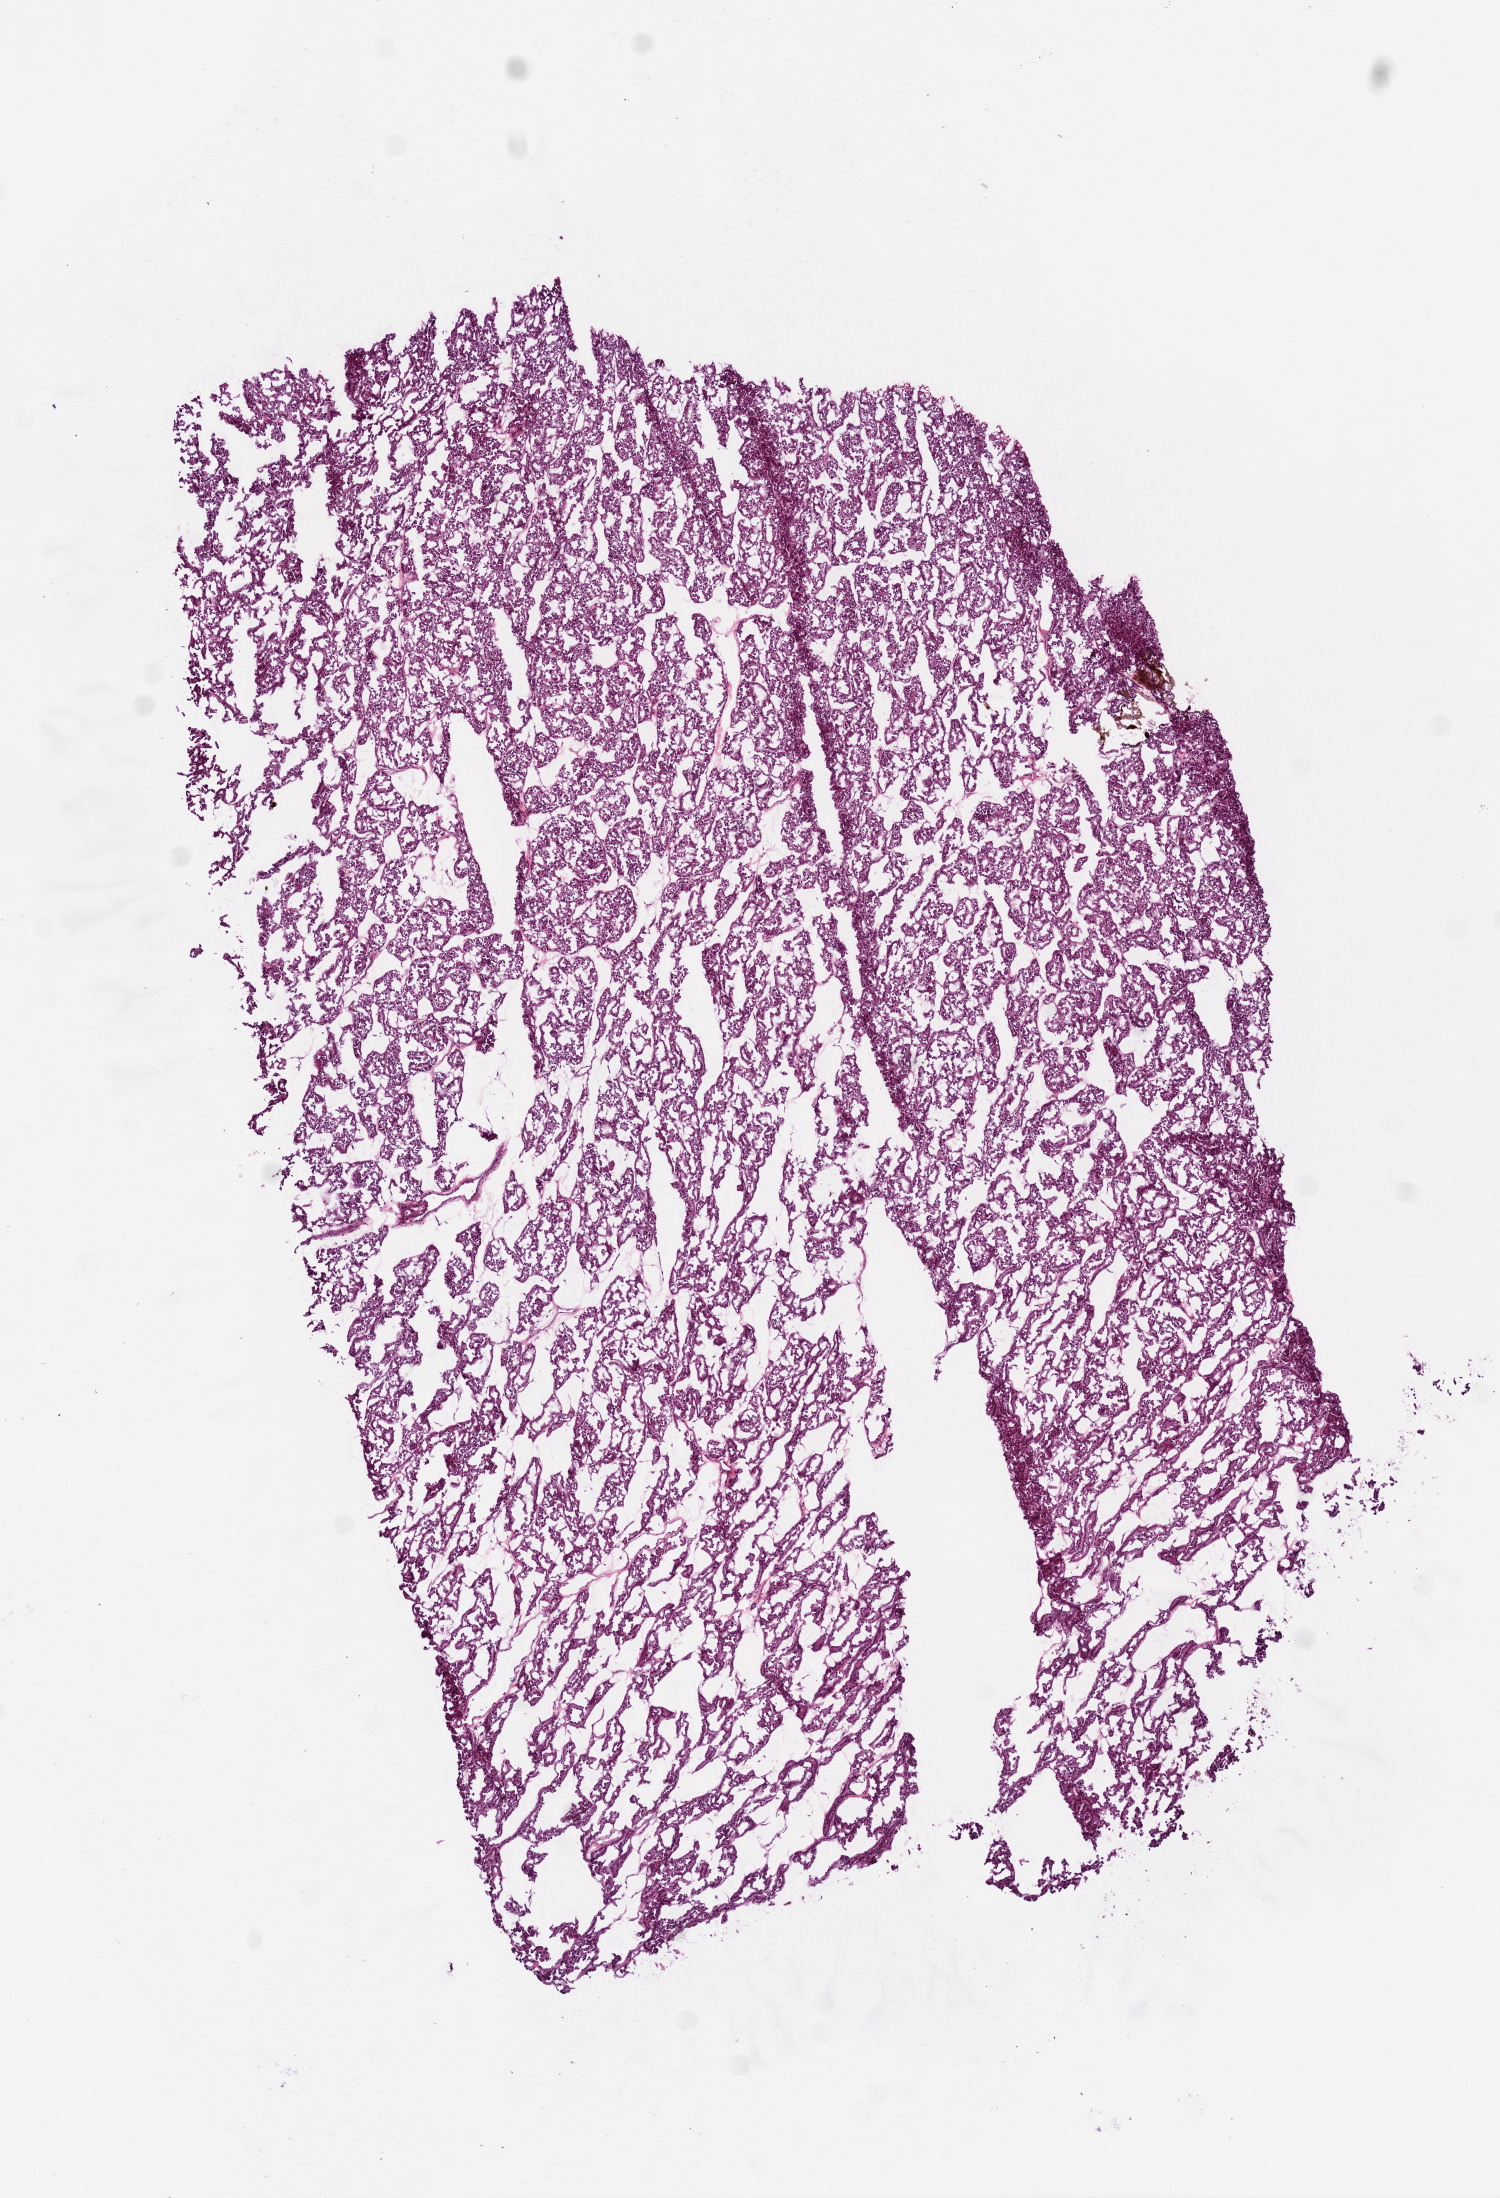
Whole-slide histology image, H&E, low-resolution overview of the scanned area, about 6.0 x 8.8 mm; frozen section from the bottom of the tissue portion; primary tumour sample from the kidney. Male, age 45 years at initial diagnosis. Histologic grade: GX (grade cannot be assessed). Slide review estimates, as recorded: tumour cells 95%, tumour nuclei 85%, normal cells 0%, stromal cells 5%, necrosis 0%.
• laterality: right
• AJCC pathologic stage: II
• pathologic diagnosis: Clear cell adenocarcinoma, NOS
• lymph nodes positive (case pathology): 0 of 7 examined